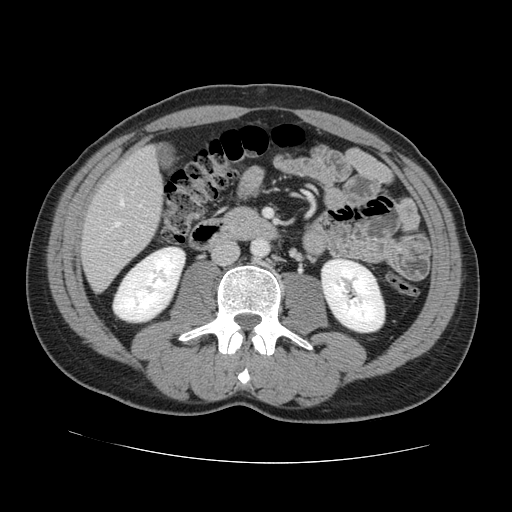
Contrast-enhanced abdominal CT, one axial slice. Slice 37 of 131 in the series (ordered by position). Soft-tissue window (W 400 / L 40 HU). 2.5 mm slice thickness. 512 × 512 image matrix, field of view 380 × 380 mm. Male patient, age 40 years. Case-level facts recorded for this patient, not image findings: diagnosis: colorectal cancer liver metastases, imaged before liver resection; multiple liver metastases: yes; largest metastasis: 2.9 cm; disease in both lobes: yes.
Outlined on this slice (outlined manually by an expert reader):
- hepatic veins: bounding box [x1, y1, x2, y2] px = [115, 200, 141, 226]
- liver: [82, 147, 162, 290]
- planned liver remnant (the part of the liver to remain after resection): [137, 148, 156, 162]
- portal vein (with intrahepatic branches): [124, 241, 127, 244]